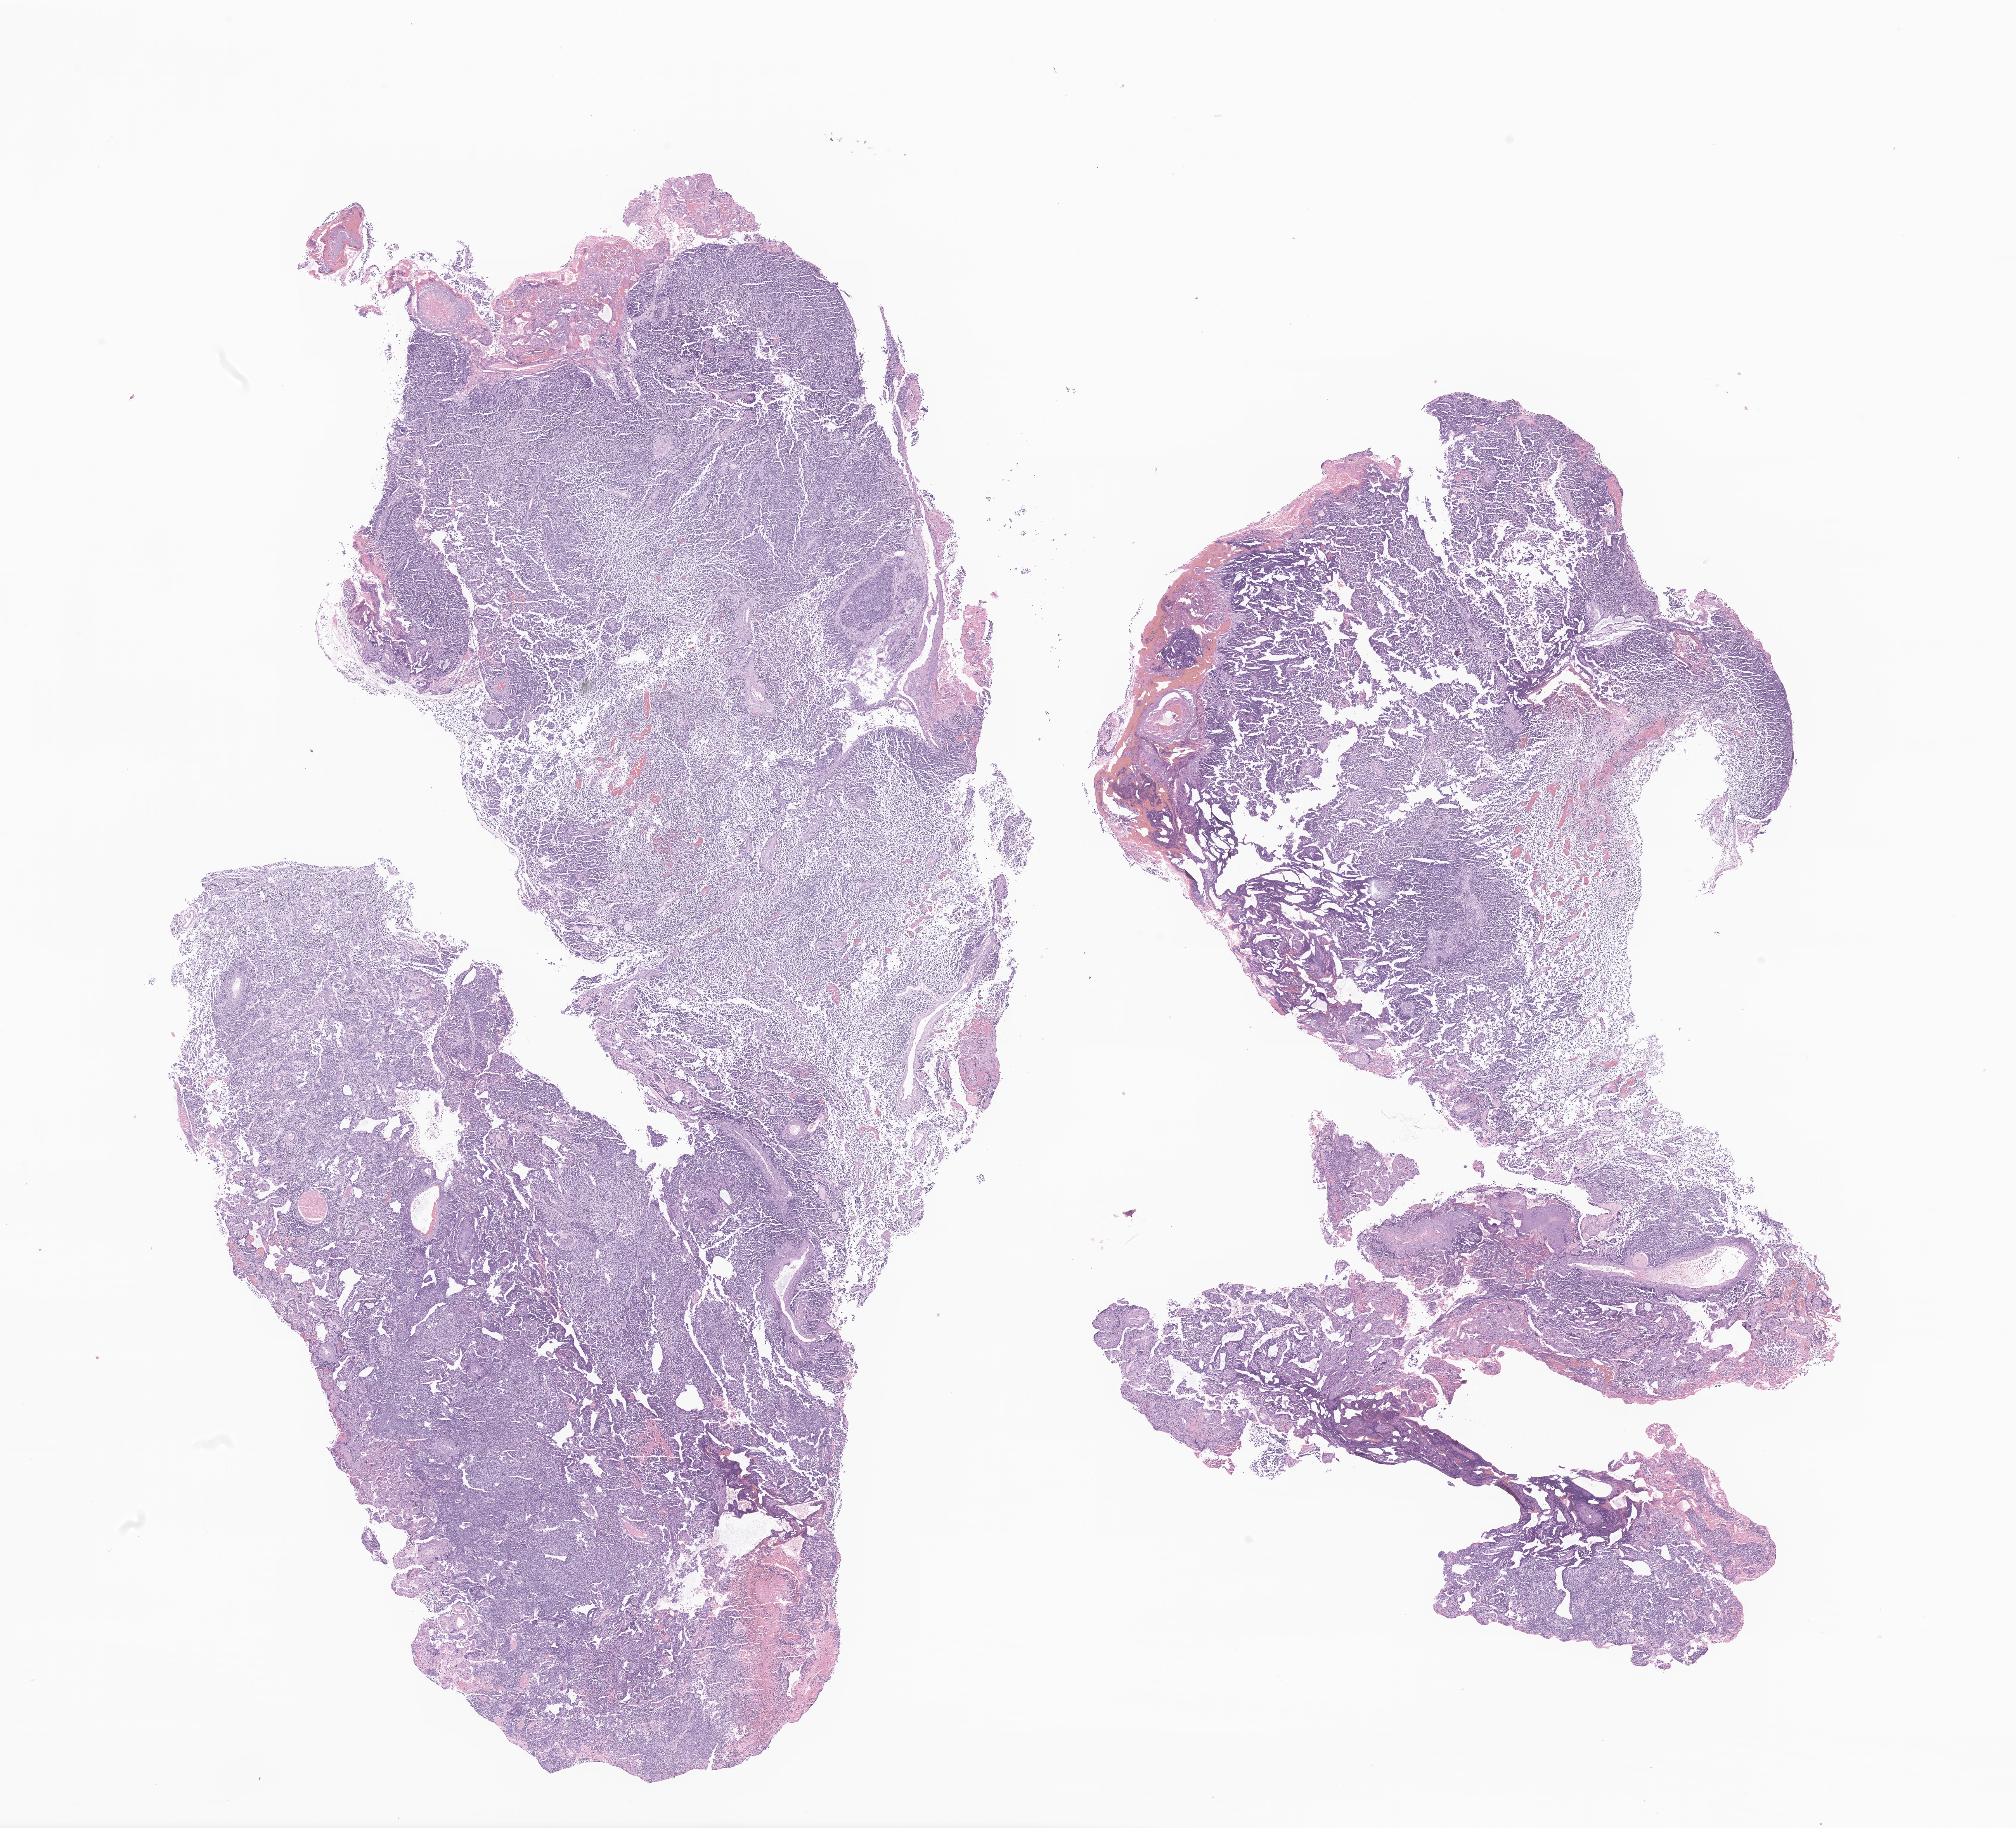
Hematoxylin and eosin (H&E) whole-slide image of tumor tissue from the brain, shown as a low-resolution overview of the whole scanned area (about 21.9 x 19.9 mm). FFPE section. Male patient, age 918 days (about 2.5 years).
* diagnosis (ICD-O-3 morphology term): Medulloblastoma, NOS